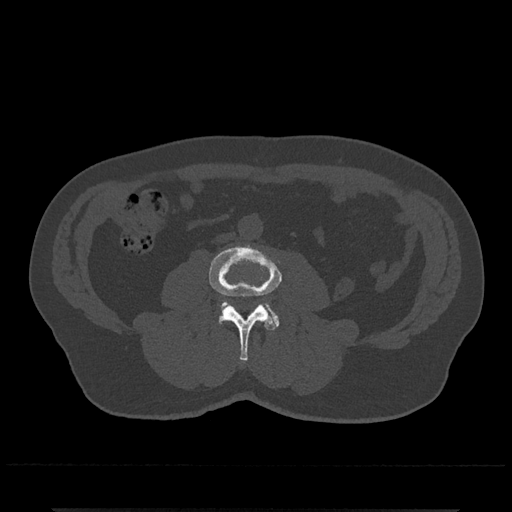
CT including the spine, one axial slice. Slice 207 of 797 in the series (ordered by position). Reconstruction kernel Br40s/3. Bone window (W 1800 / L 400 HU). 0.5 mm slice thickness. 512 × 512 image matrix, field of view 393 × 393 mm. Male patient, age 67 years. From the clinical record (not read from this slice): primary cancer: prostate.
Annotated regions visible in this slice (semi-automatic segmentation, software-assisted and operator-edited):
- L3 vertebra: bounding box <208,245,282,361> (left, top, right, bottom; pixels)
- L4 vertebra: <221,301,279,327>